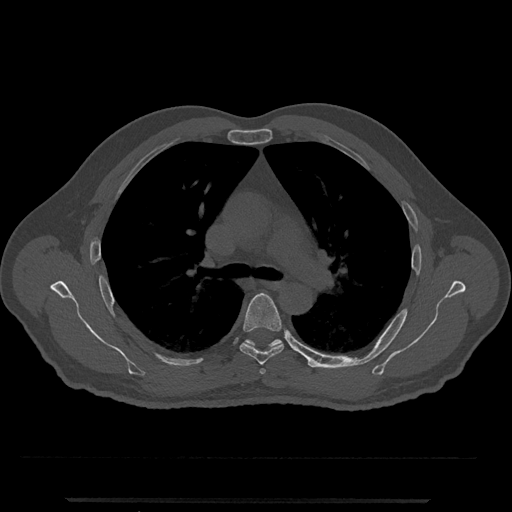
CT including the spine, one axial slice. Position 781 of 797 along the scan axis. Bone window (W 1800 / L 400 HU). 512 × 512 image matrix, field of view 419 × 419 mm. Male patient, age 63 years. From the clinical record (not read from this slice): primary cancer: prostate.
Annotated regions visible in this slice (semi-automatic segmentation, software-assisted and operator-edited):
- T5 vertebra: bounding box <239,293,284,365> (left, top, right, bottom; pixels)
- T6 vertebra: <244,339,282,347>